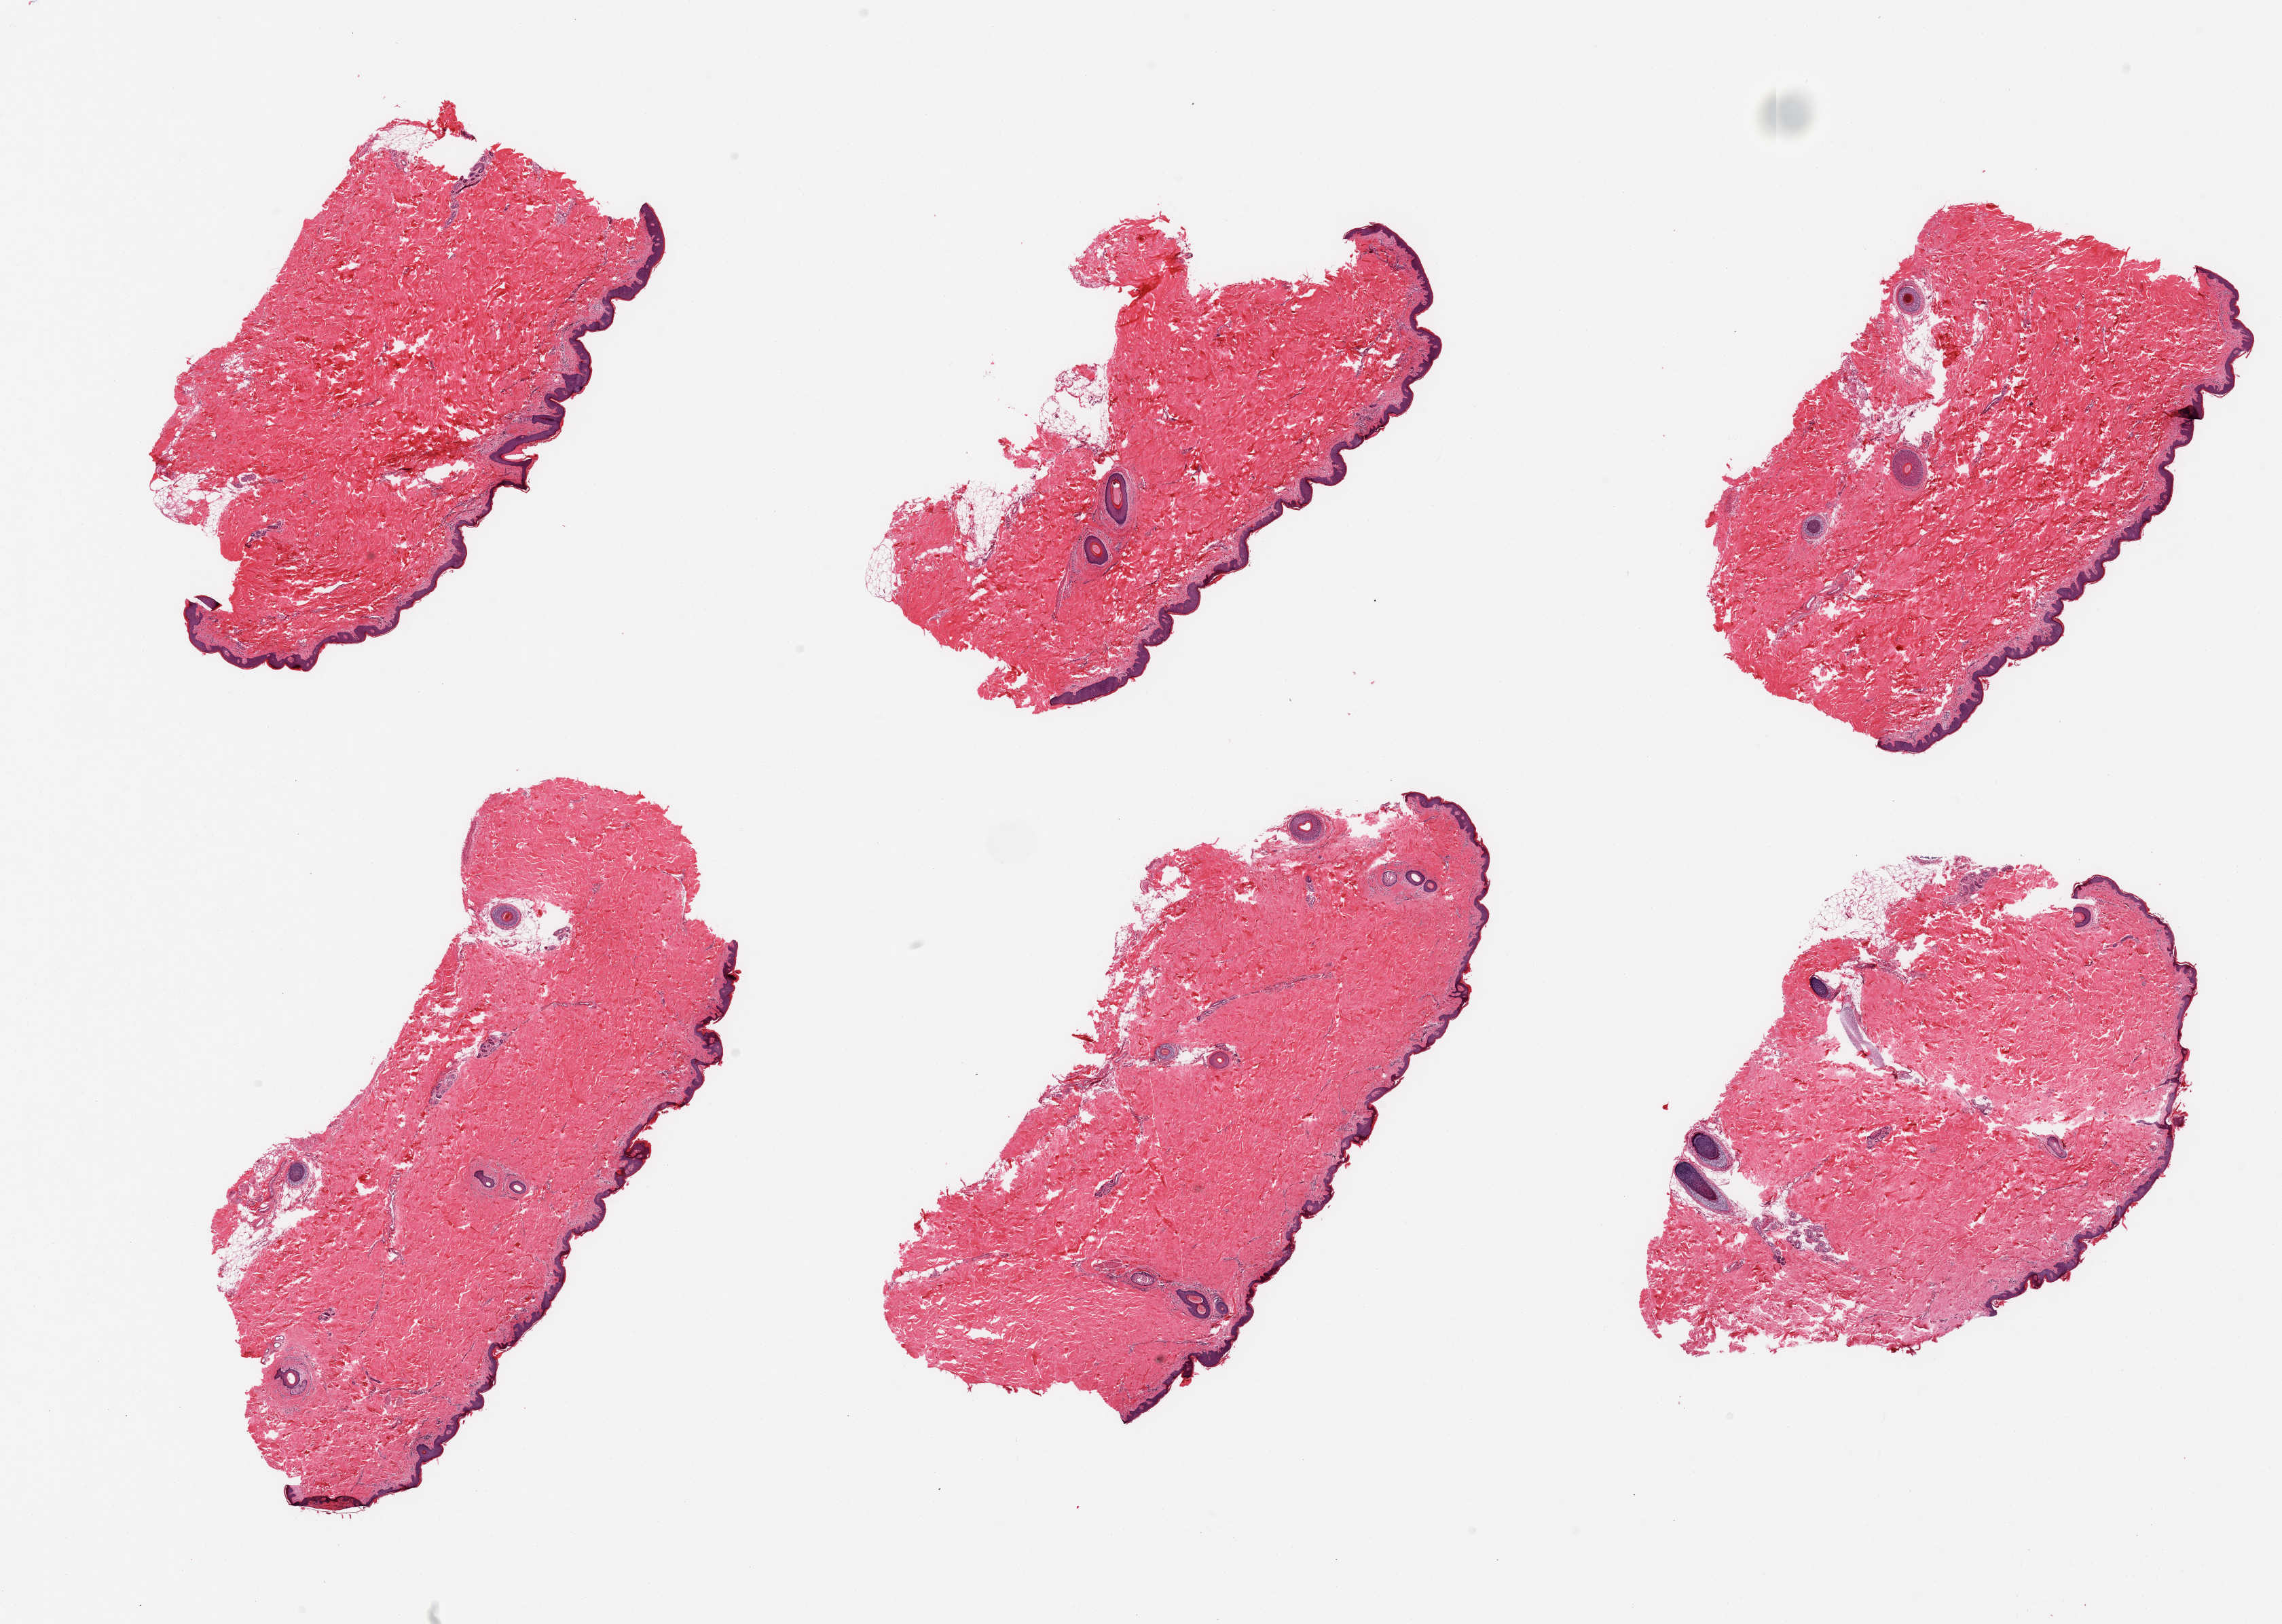
Whole-slide image, H&E stain, brightfield, whole scanned area (about 26.6 x 18.9 mm) shown as a low-resolution overview, PAXgene-fixed paraffin-embedded (PFPE) section, section of skin of suprapubic region (target tissue), donor tissue sample. Donor sex: male.
Review note (as recorded): 6 pieces; well trimmed, hair-bearing skin; 5% dermal fat.